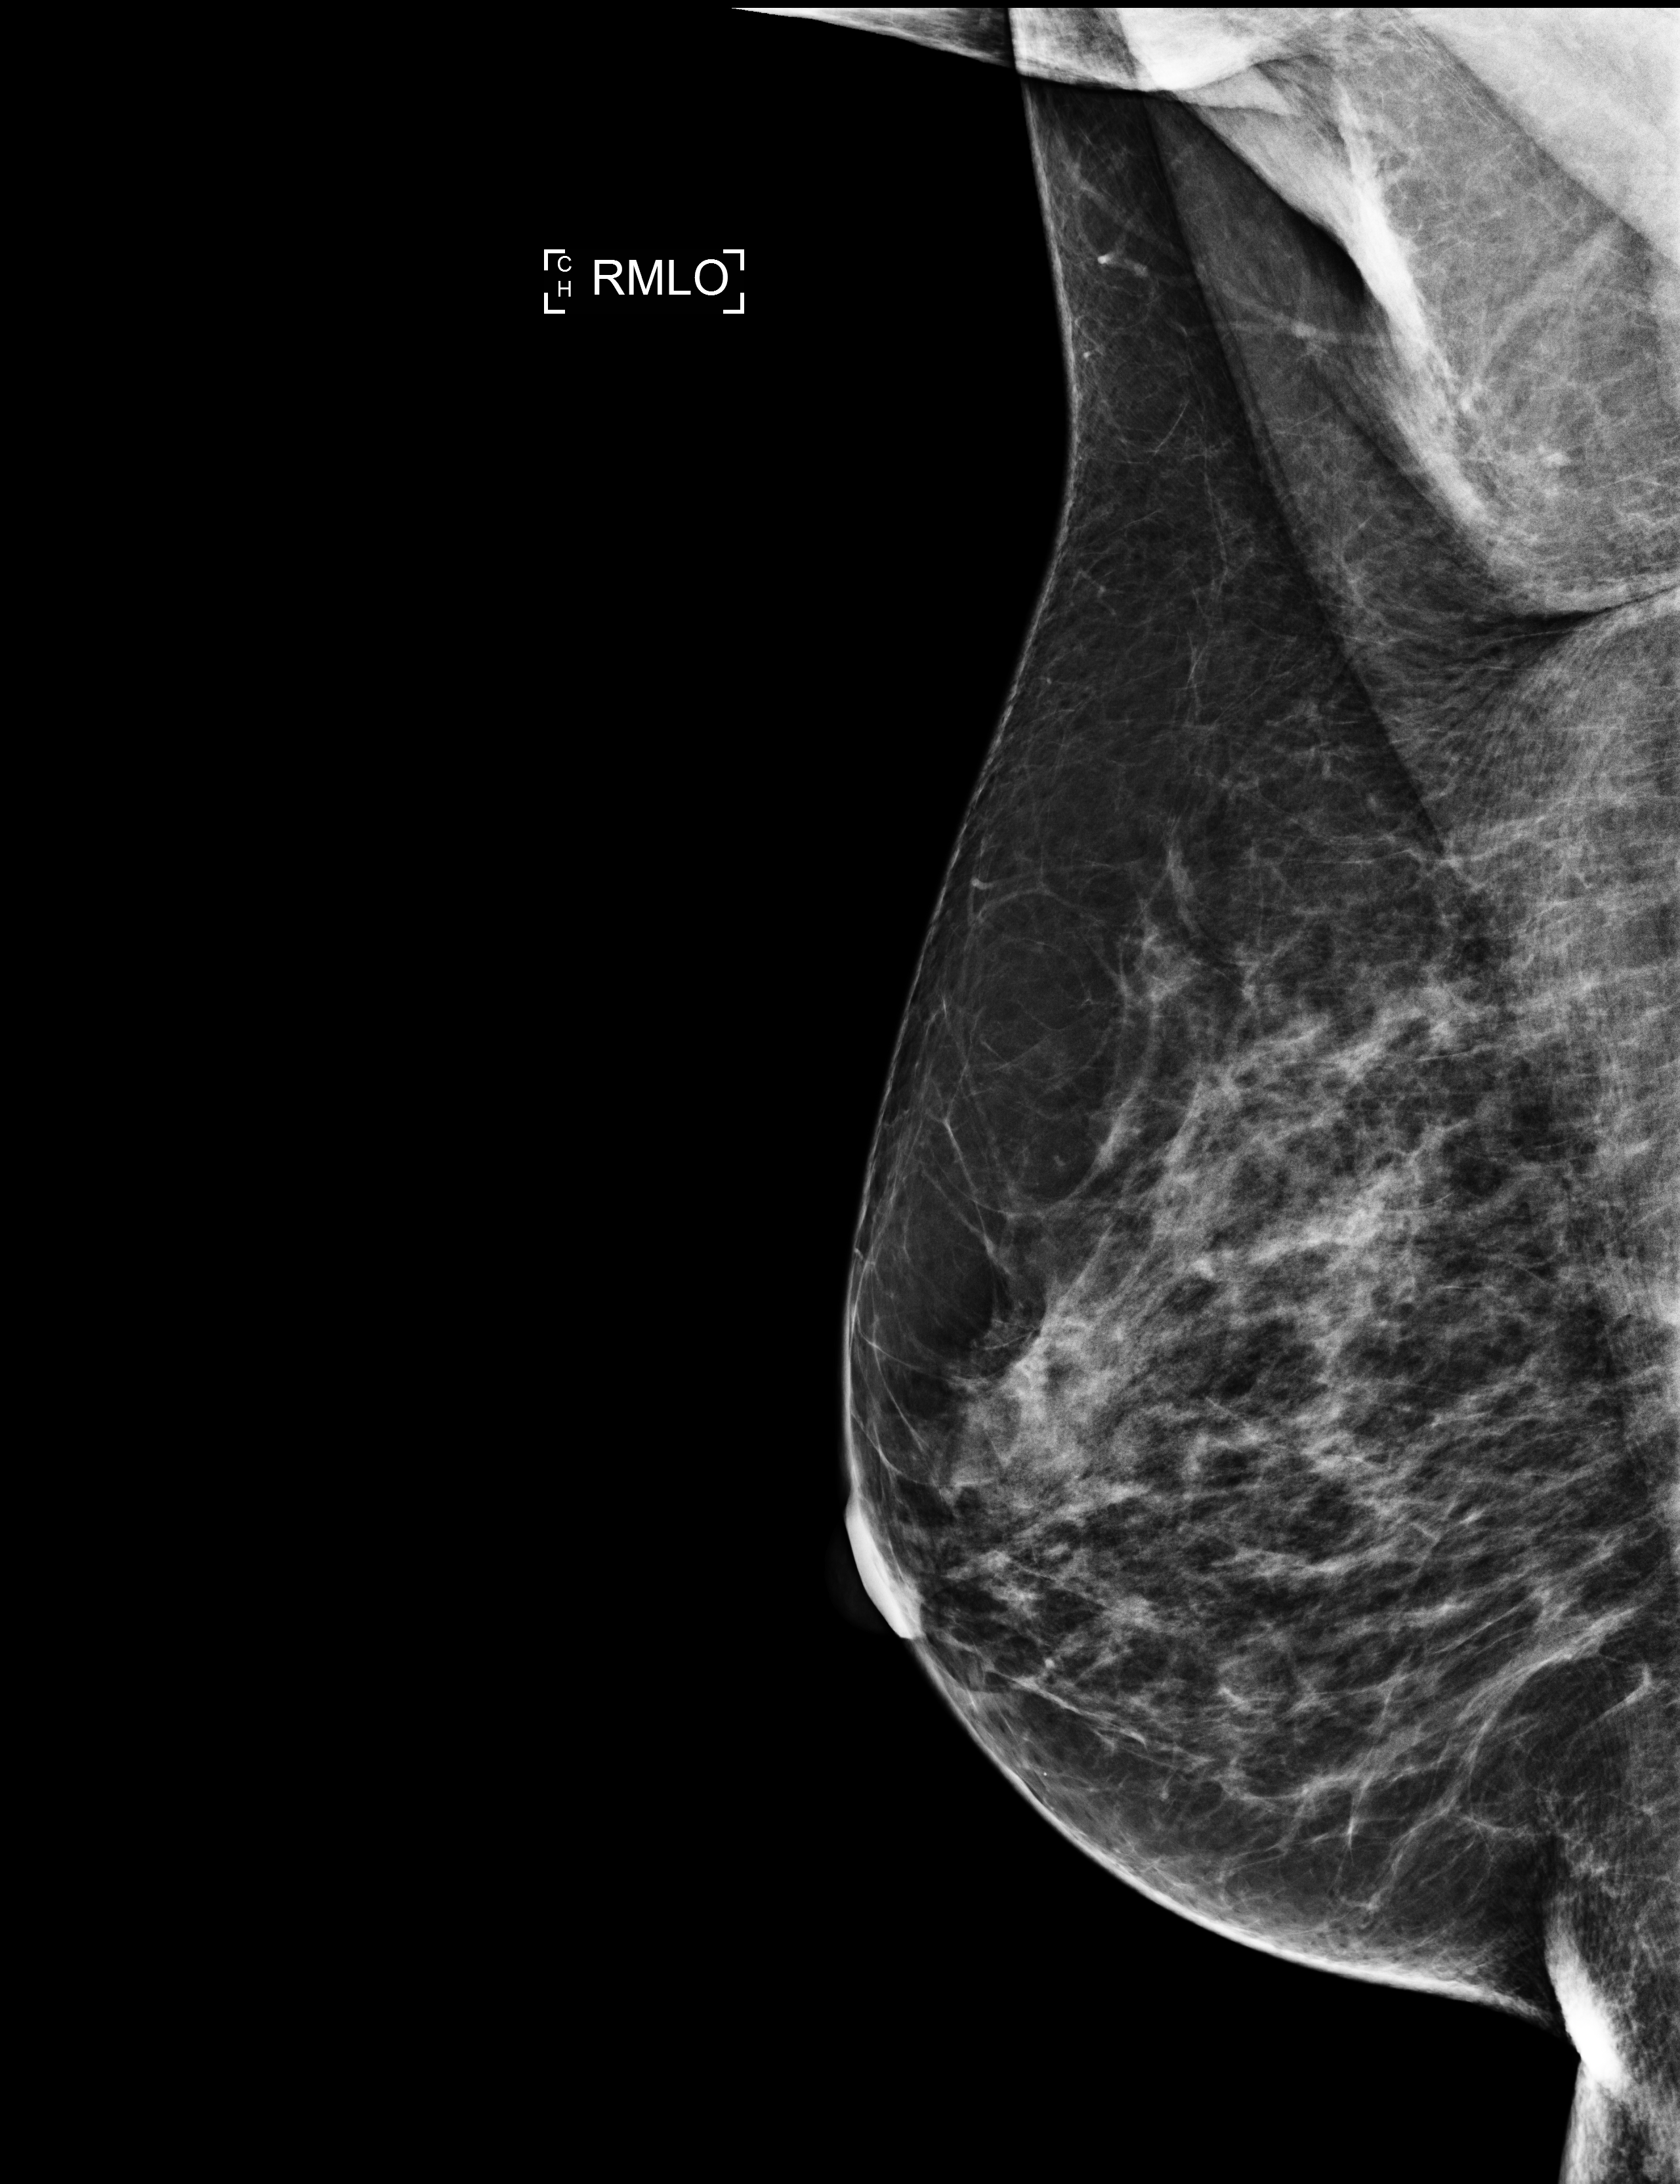
Screening examination, system: Selenia Dimensions. Female patient, age 60 years.
Image type: full-field digital mammogram. Breast: right. Projection: MLO view.